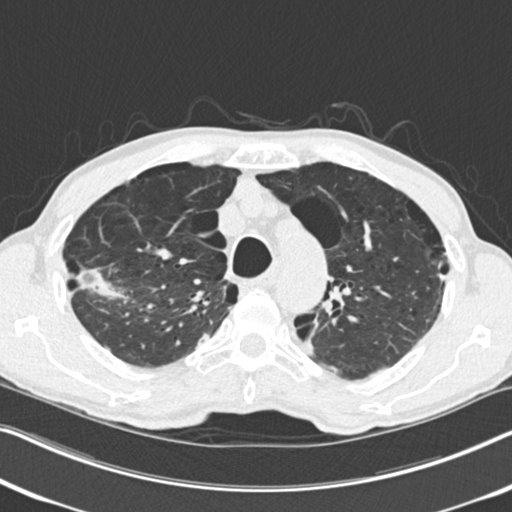
Low-dose screening chest CT, one axial slice; slice 190 of 251 in the series (ordered by position); 120 kVp; lung window (W 1500 / L -600 HU); 2 mm slice thickness; 512 × 512 image matrix.
Outlined on this slice (expert manual segmentation):
- lesion 1 (tumor, upper lobe of right lung): bounding box (x1, y1, x2, y2) in pixels: (77, 268, 126, 300)